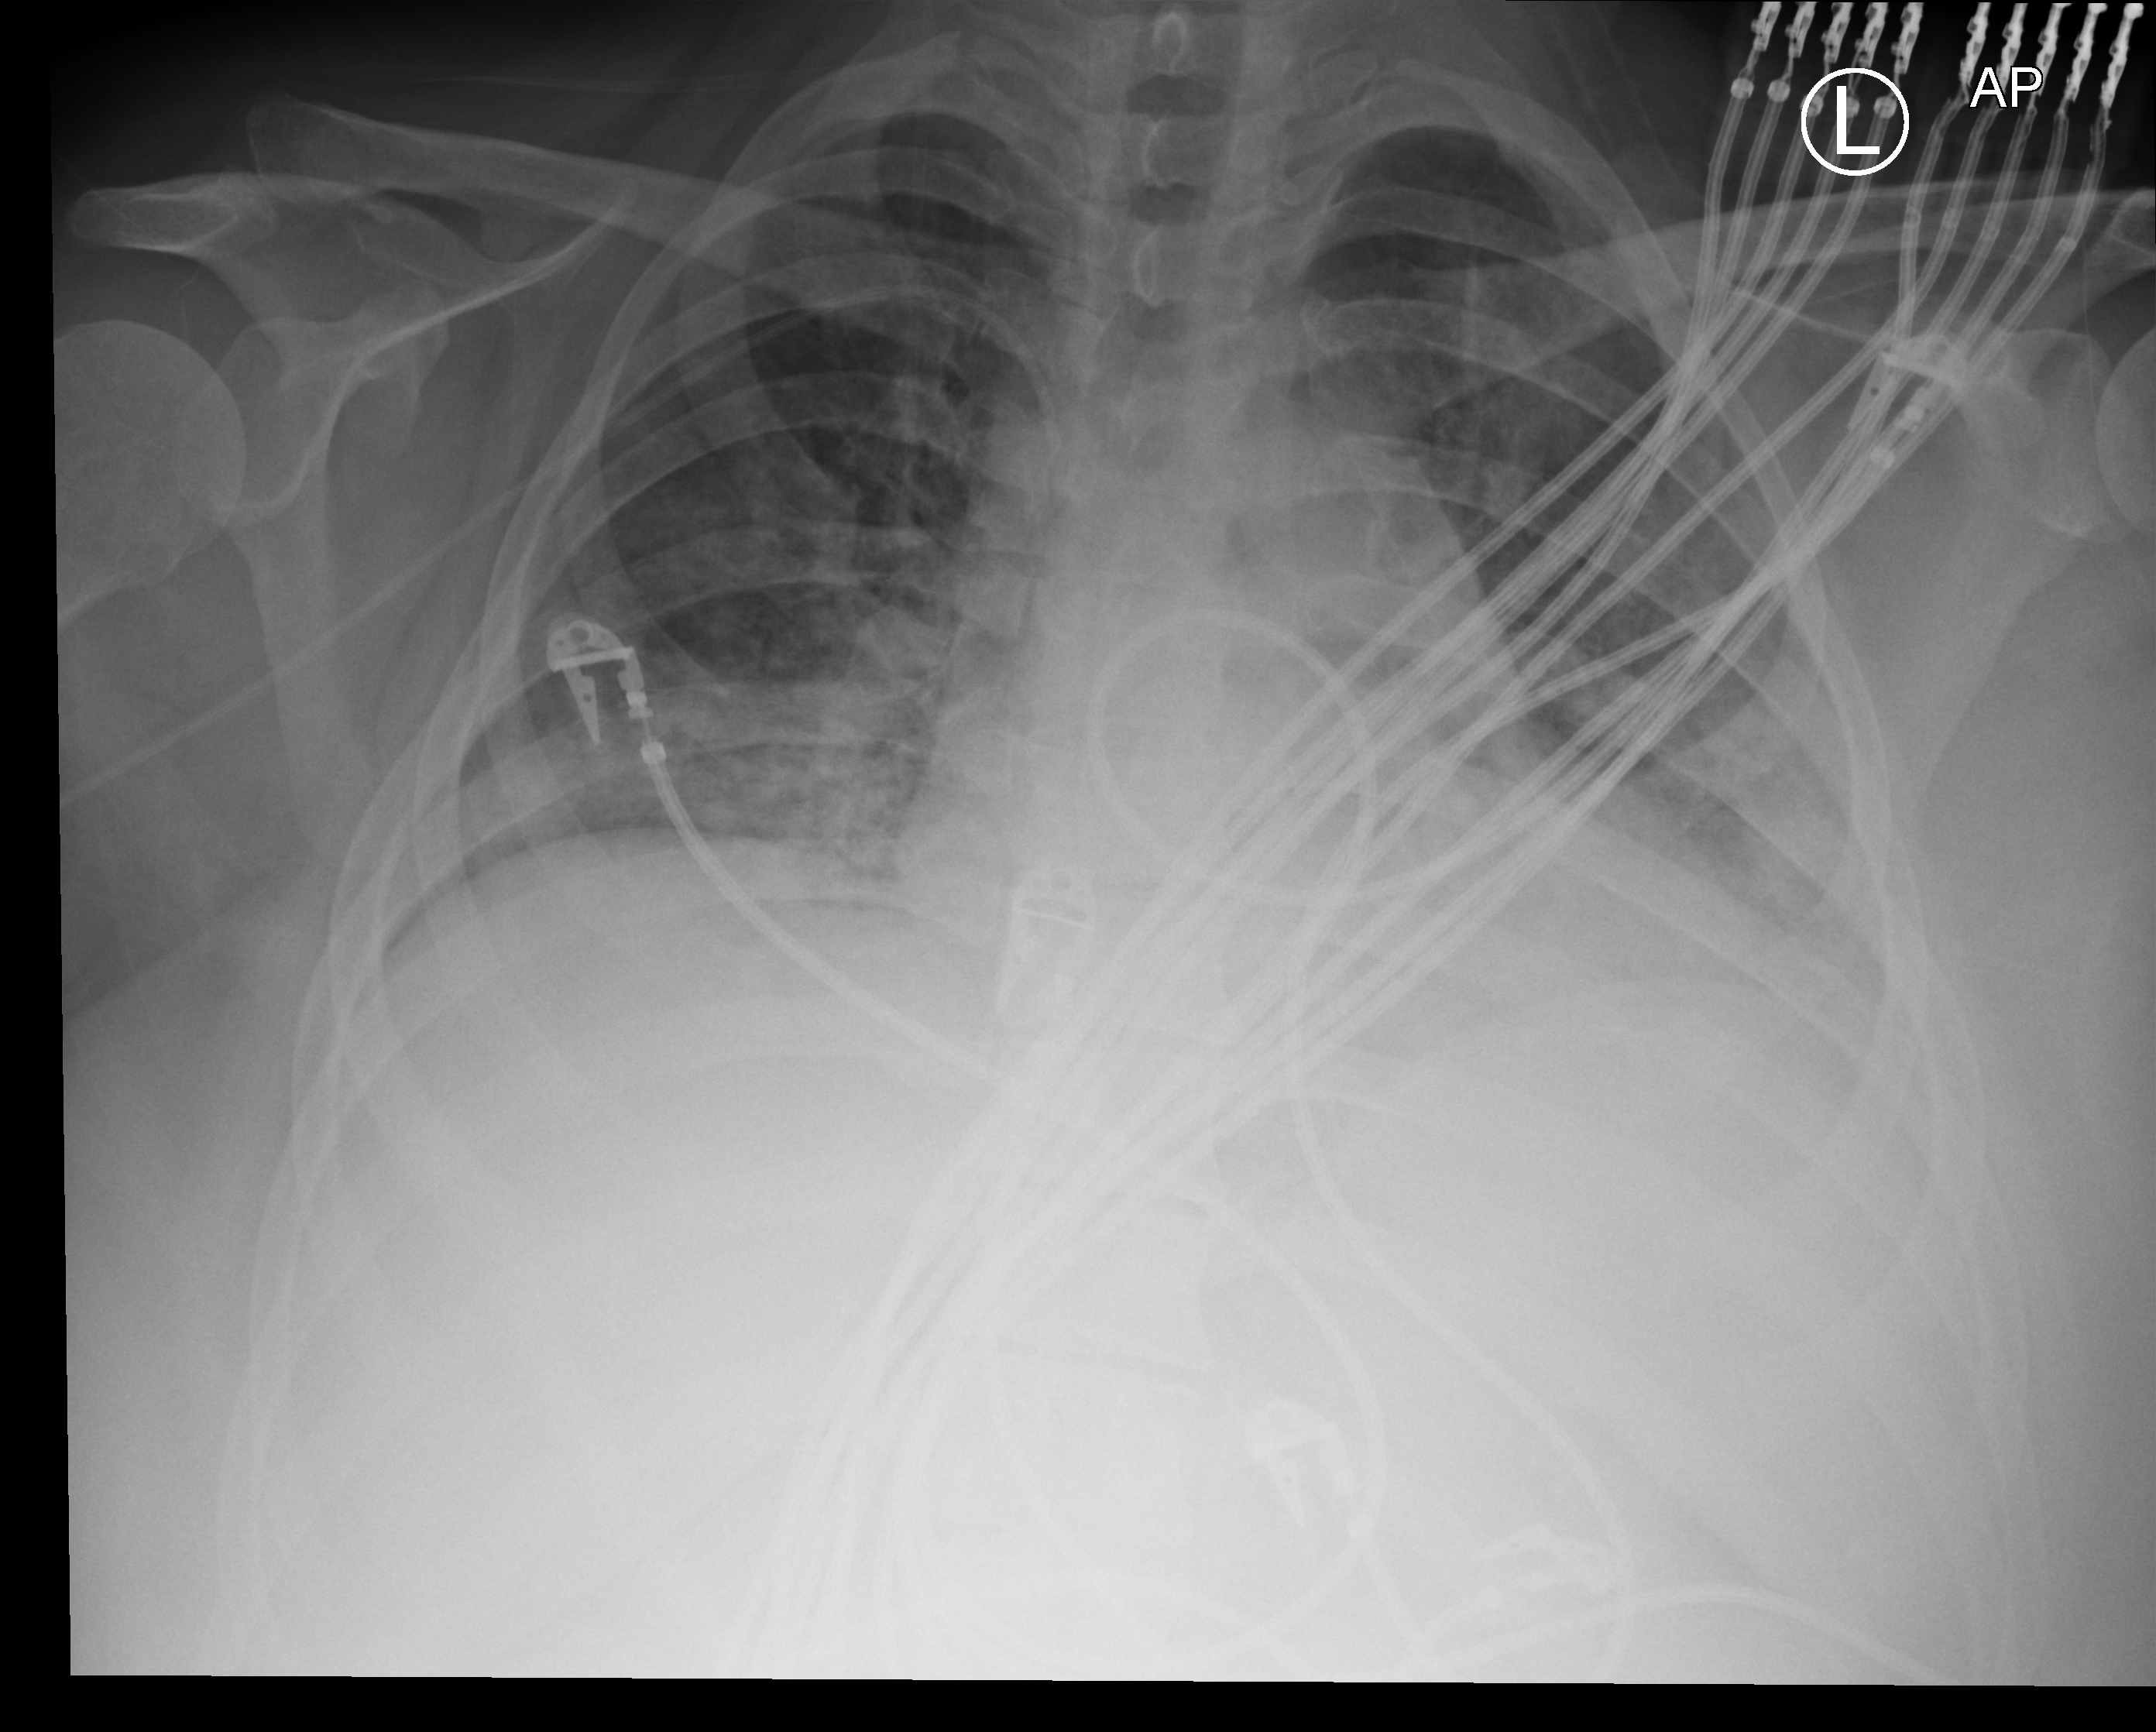
Portable chest radiograph, anteroposterior (AP) projection. Female patient hospitalised with COVID-19, age 18–59 years.
Admission-level facts for this patient (not findings on this image; timing relative to this image not recorded): mechanically ventilated during this hospital stay: yes; smoking status (admission record): never; admitted to intensive care during this hospital stay: yes.